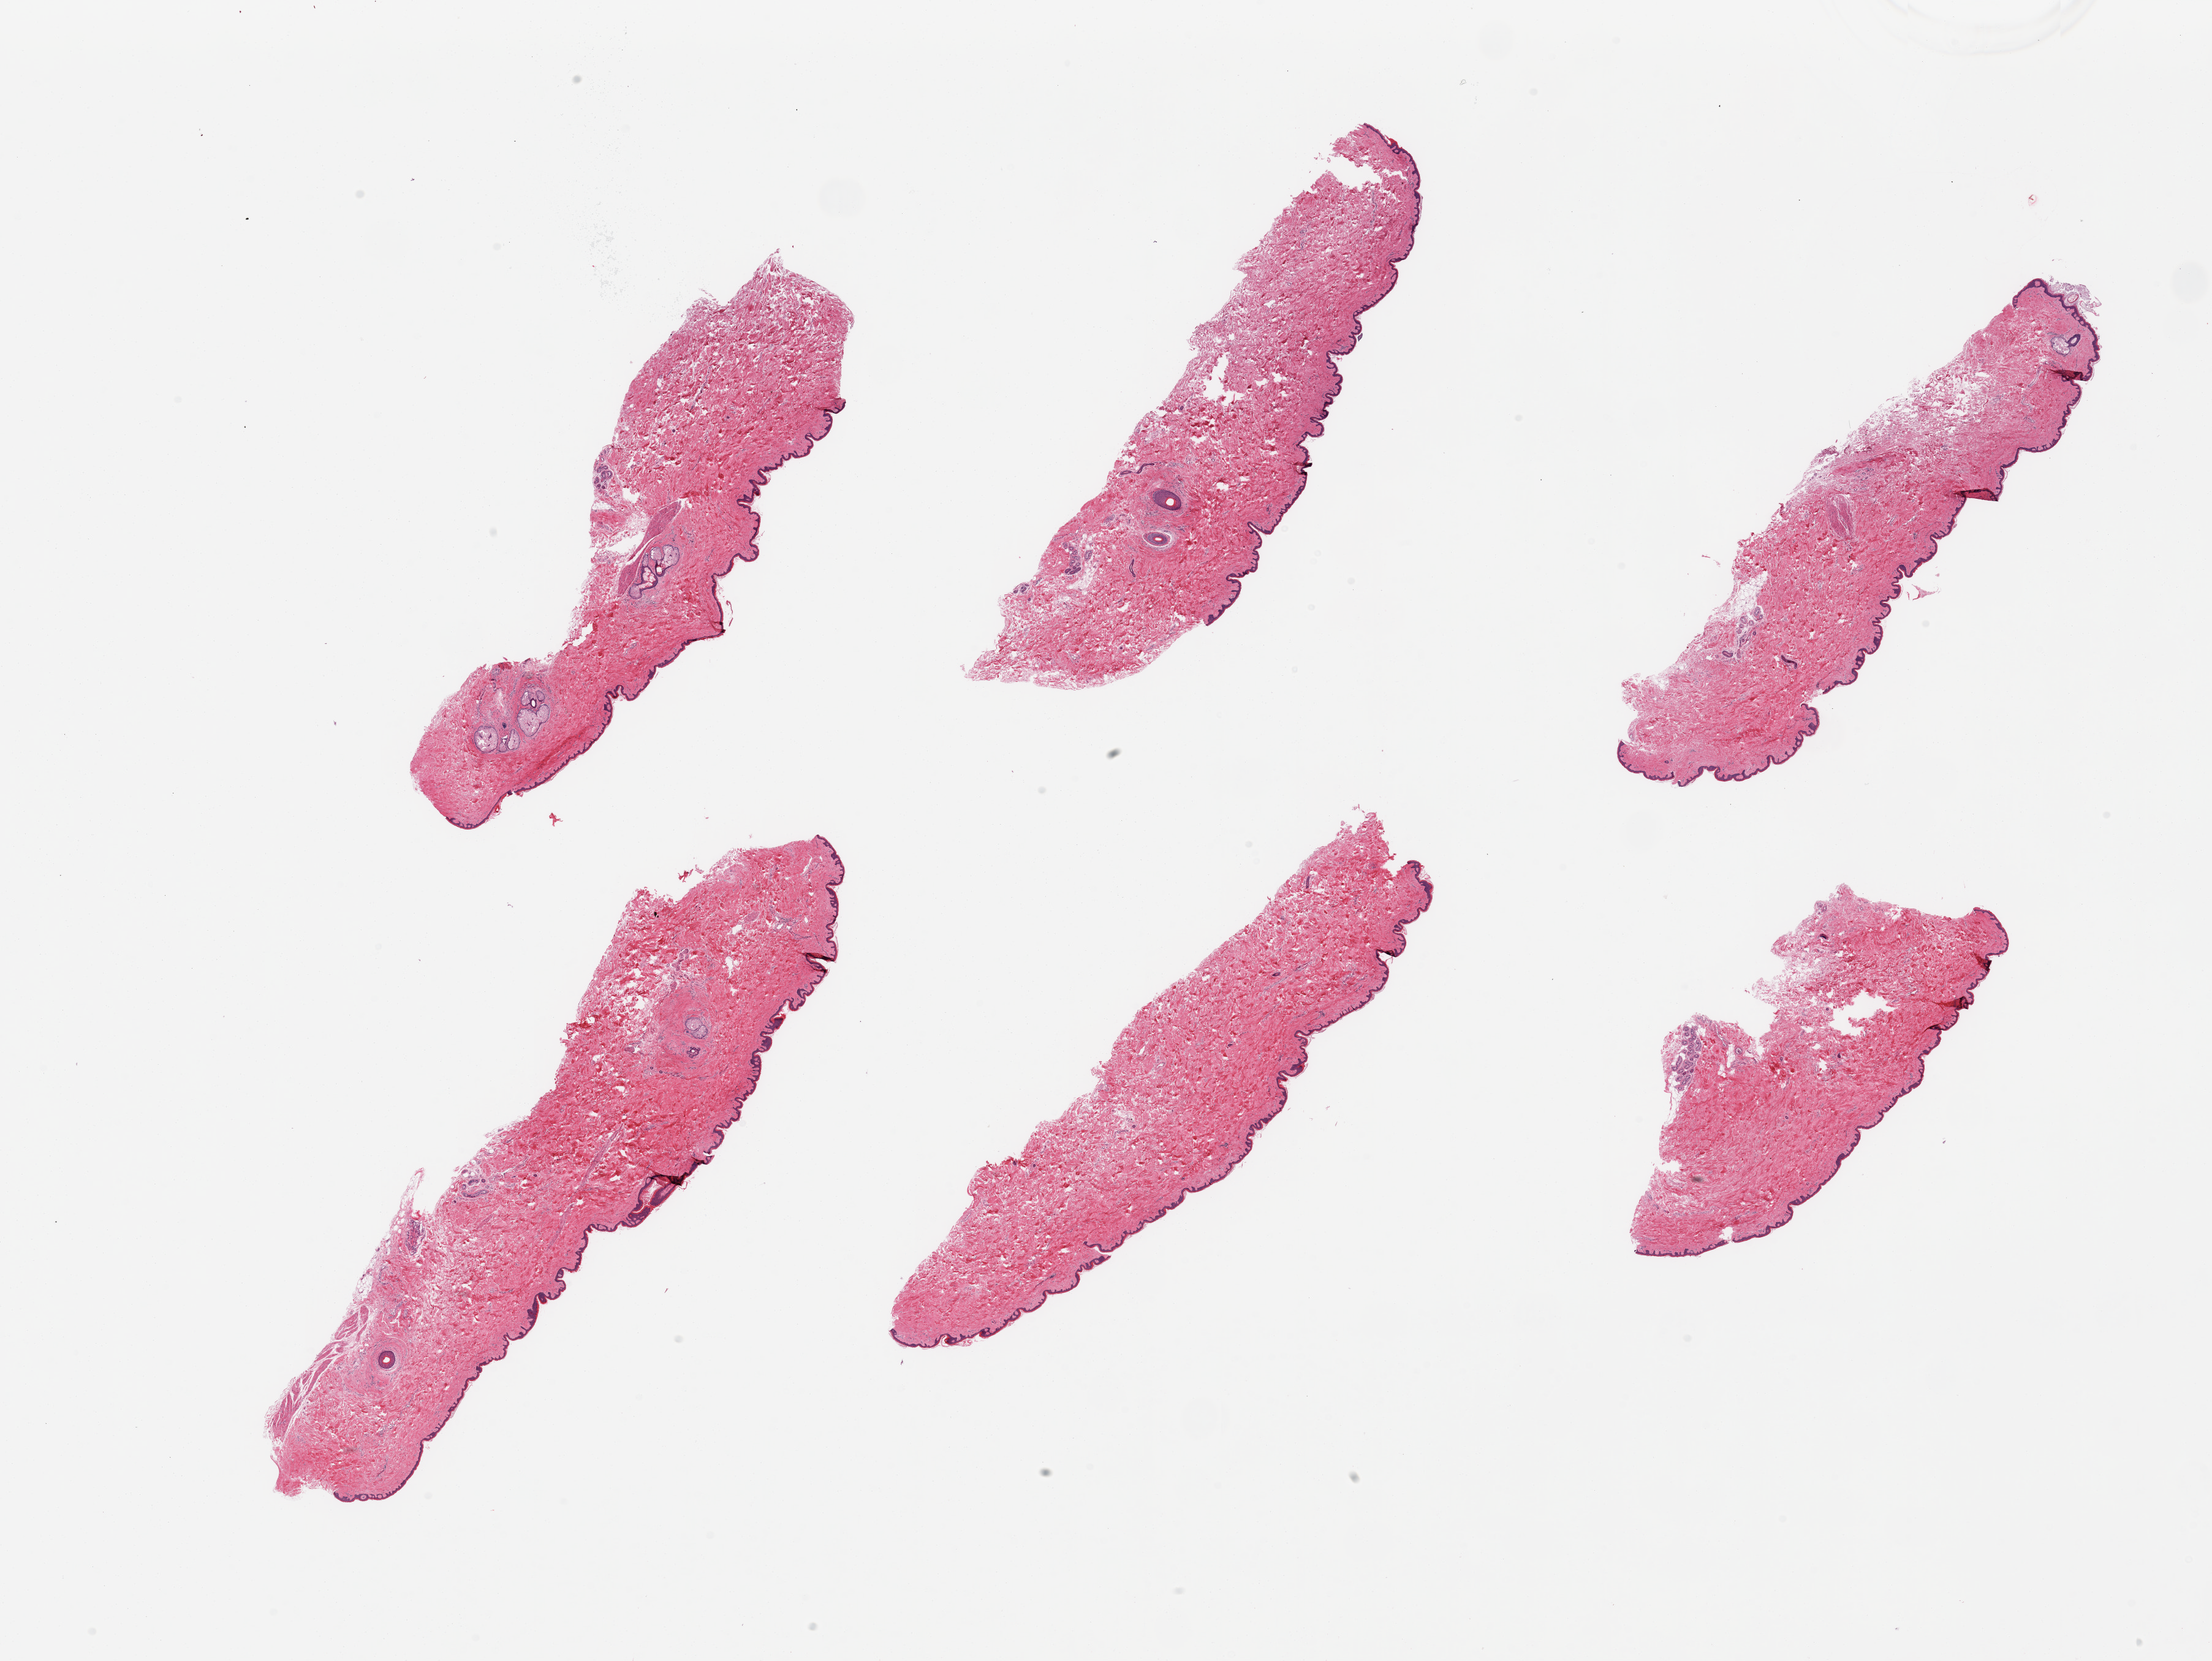
Whole-slide image, haematoxylin and eosin stain, brightfield, whole scanned area (about 28.5 x 21.4 mm, from a 20x scan) shown as a low-resolution overview; PAXgene-fixed, paraffin-embedded tissue; section of skin of suprapubic region (target tissue); donor tissue sample. Donor: male.
• reviewer comment on this tissue sample: 6 pieces; dermal fat 5%; well dissected